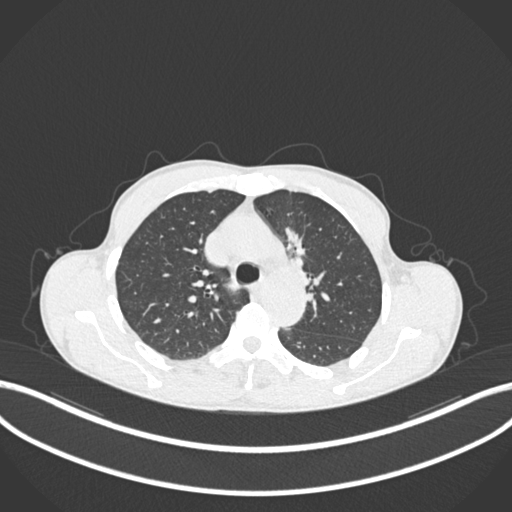
Chest CT, one axial slice; position 139 of 211 along the scan axis; 120 kVp; lung window (W 1500 / L -600 HU); 1 mm slice thickness; 512 × 512 image matrix. Male patient, age 58 years. Case-level facts recorded for this patient, not image findings: clinical TNM (as recorded): T1c N1 M0.
Structures marked on this image (rectangle marked by the reading radiologist):
- lung tumour (recorded histology: adenocarcinoma): bounding box (x1, y1, x2, y2) in pixels: (277, 223, 314, 279)